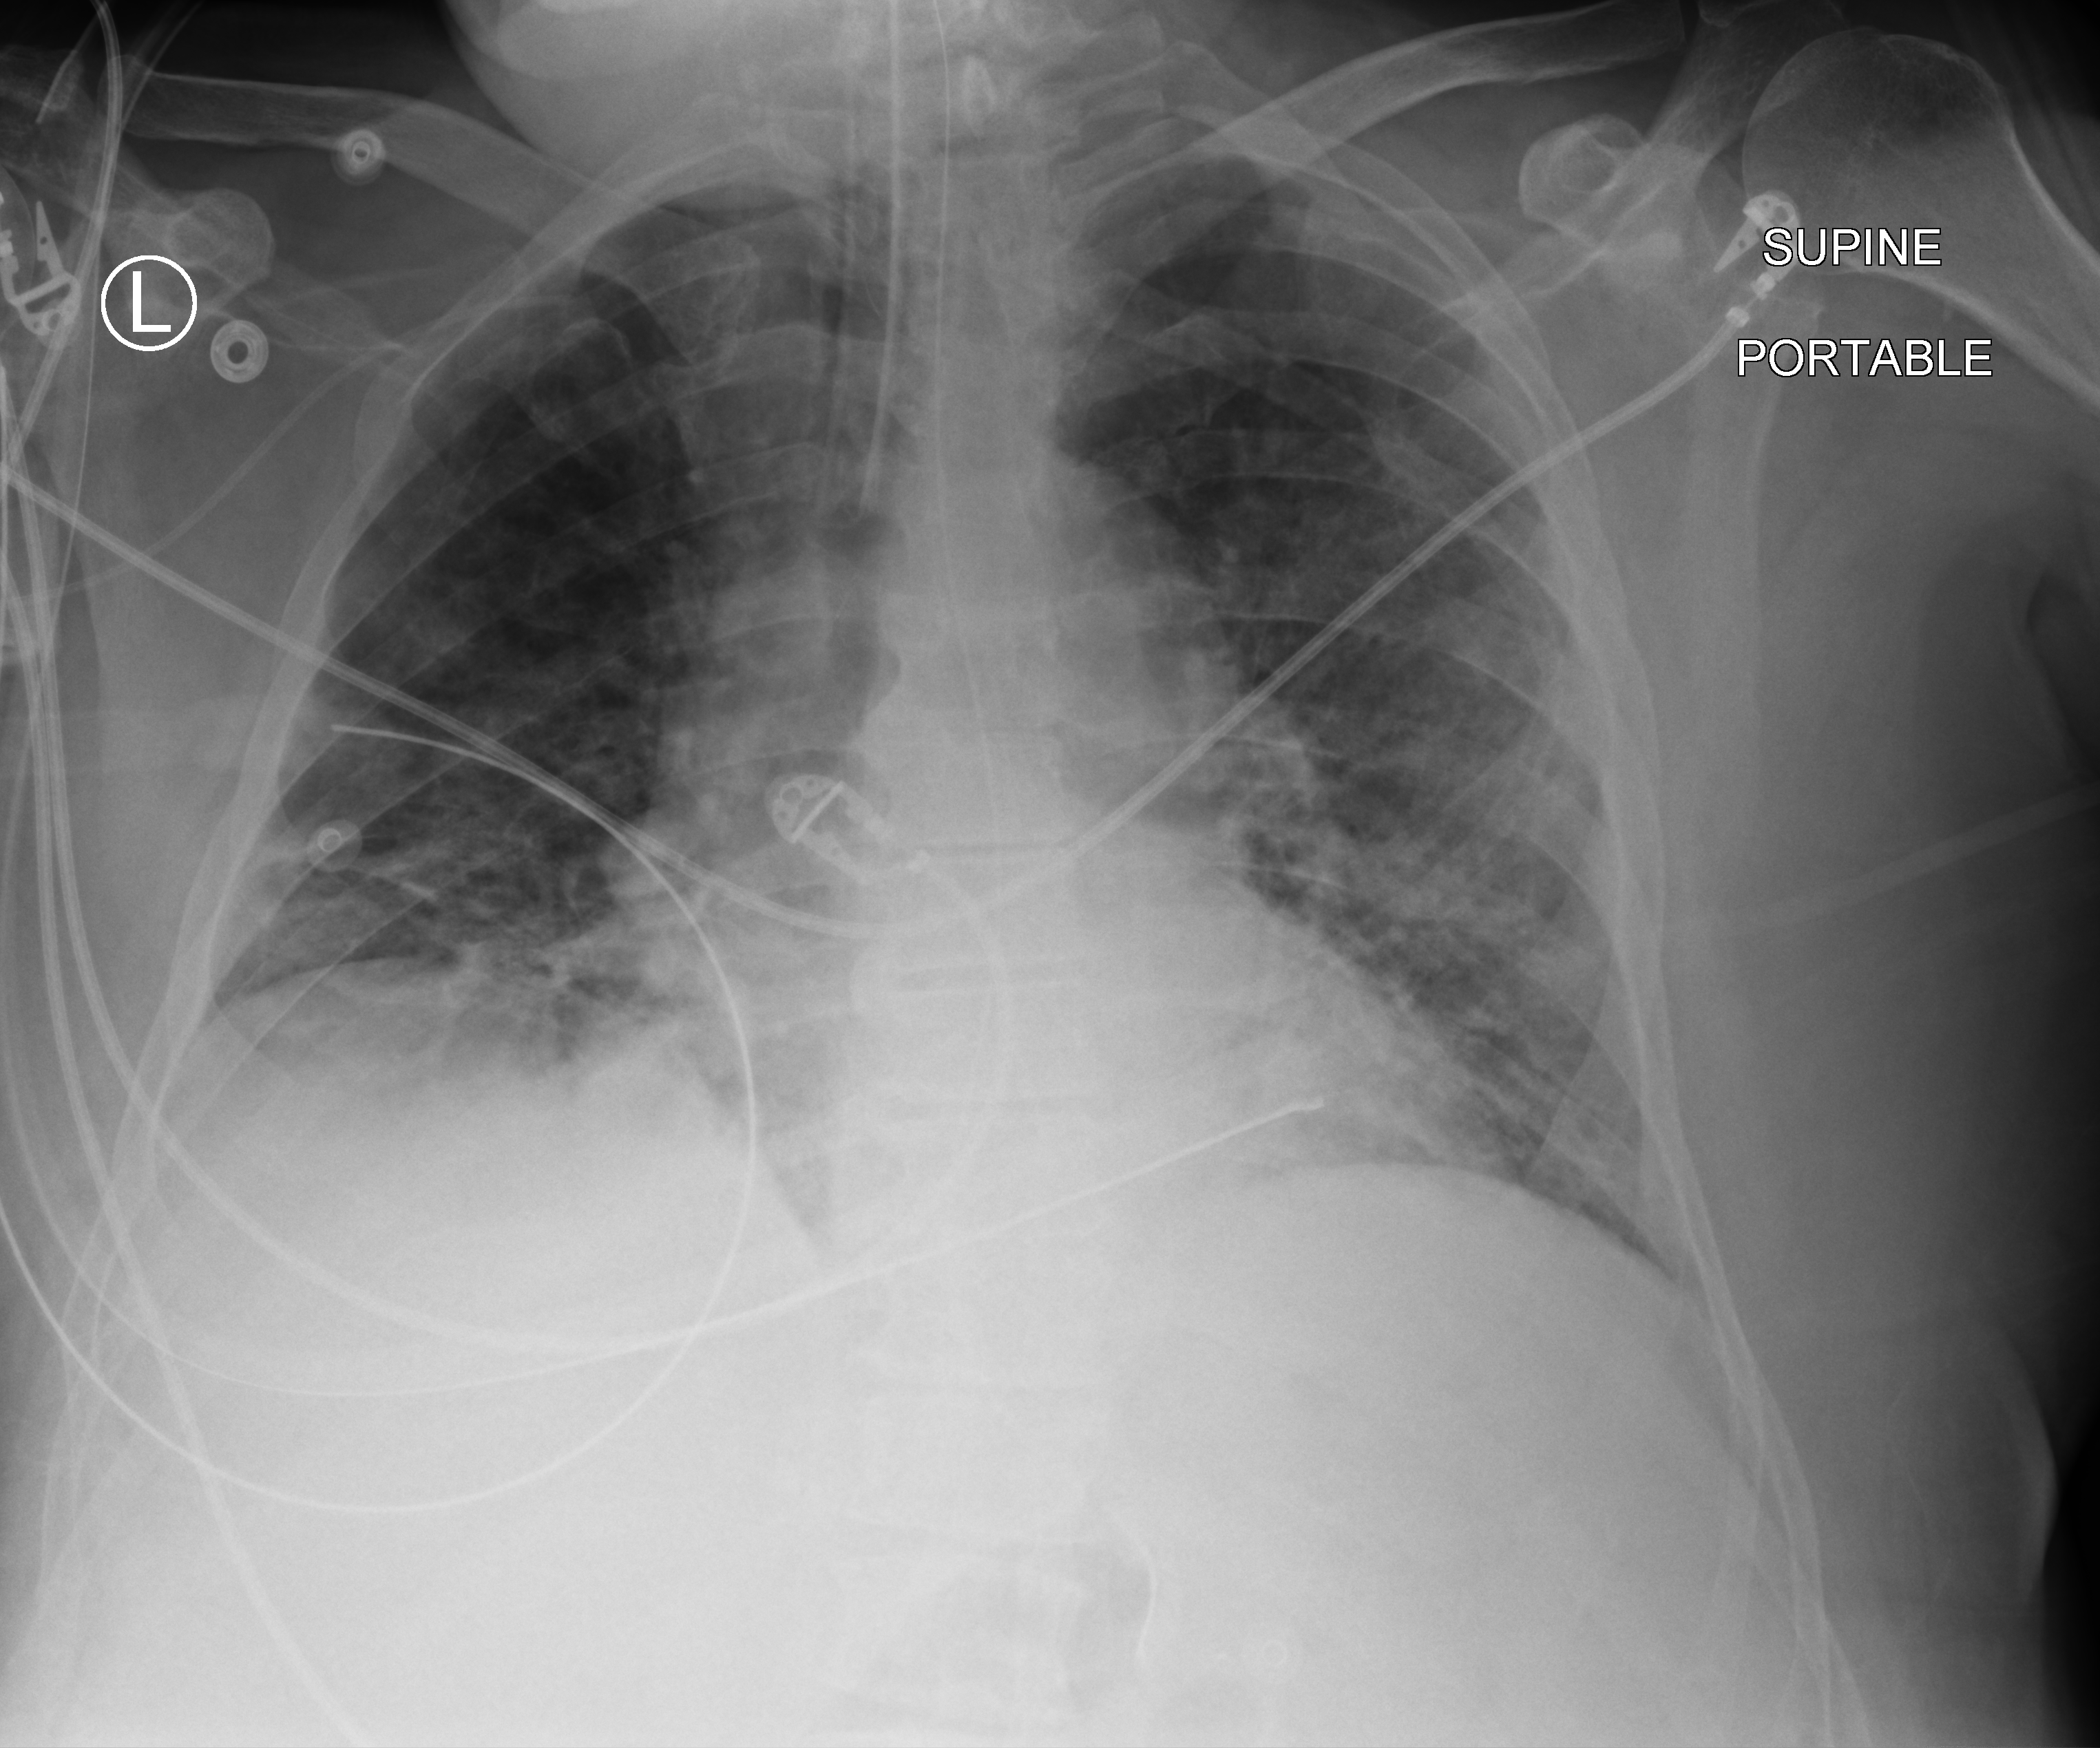
Chest X-ray (portable), anteroposterior (AP) projection. Patient hospitalised with COVID-19; male, aged 60–74 years.
From the hospital-stay record, not from the radiograph (when in the stay this image was taken is not recorded): length of hospital stay: 26 days; diabetes (admission record): no; mechanically ventilated during this hospital stay: yes.